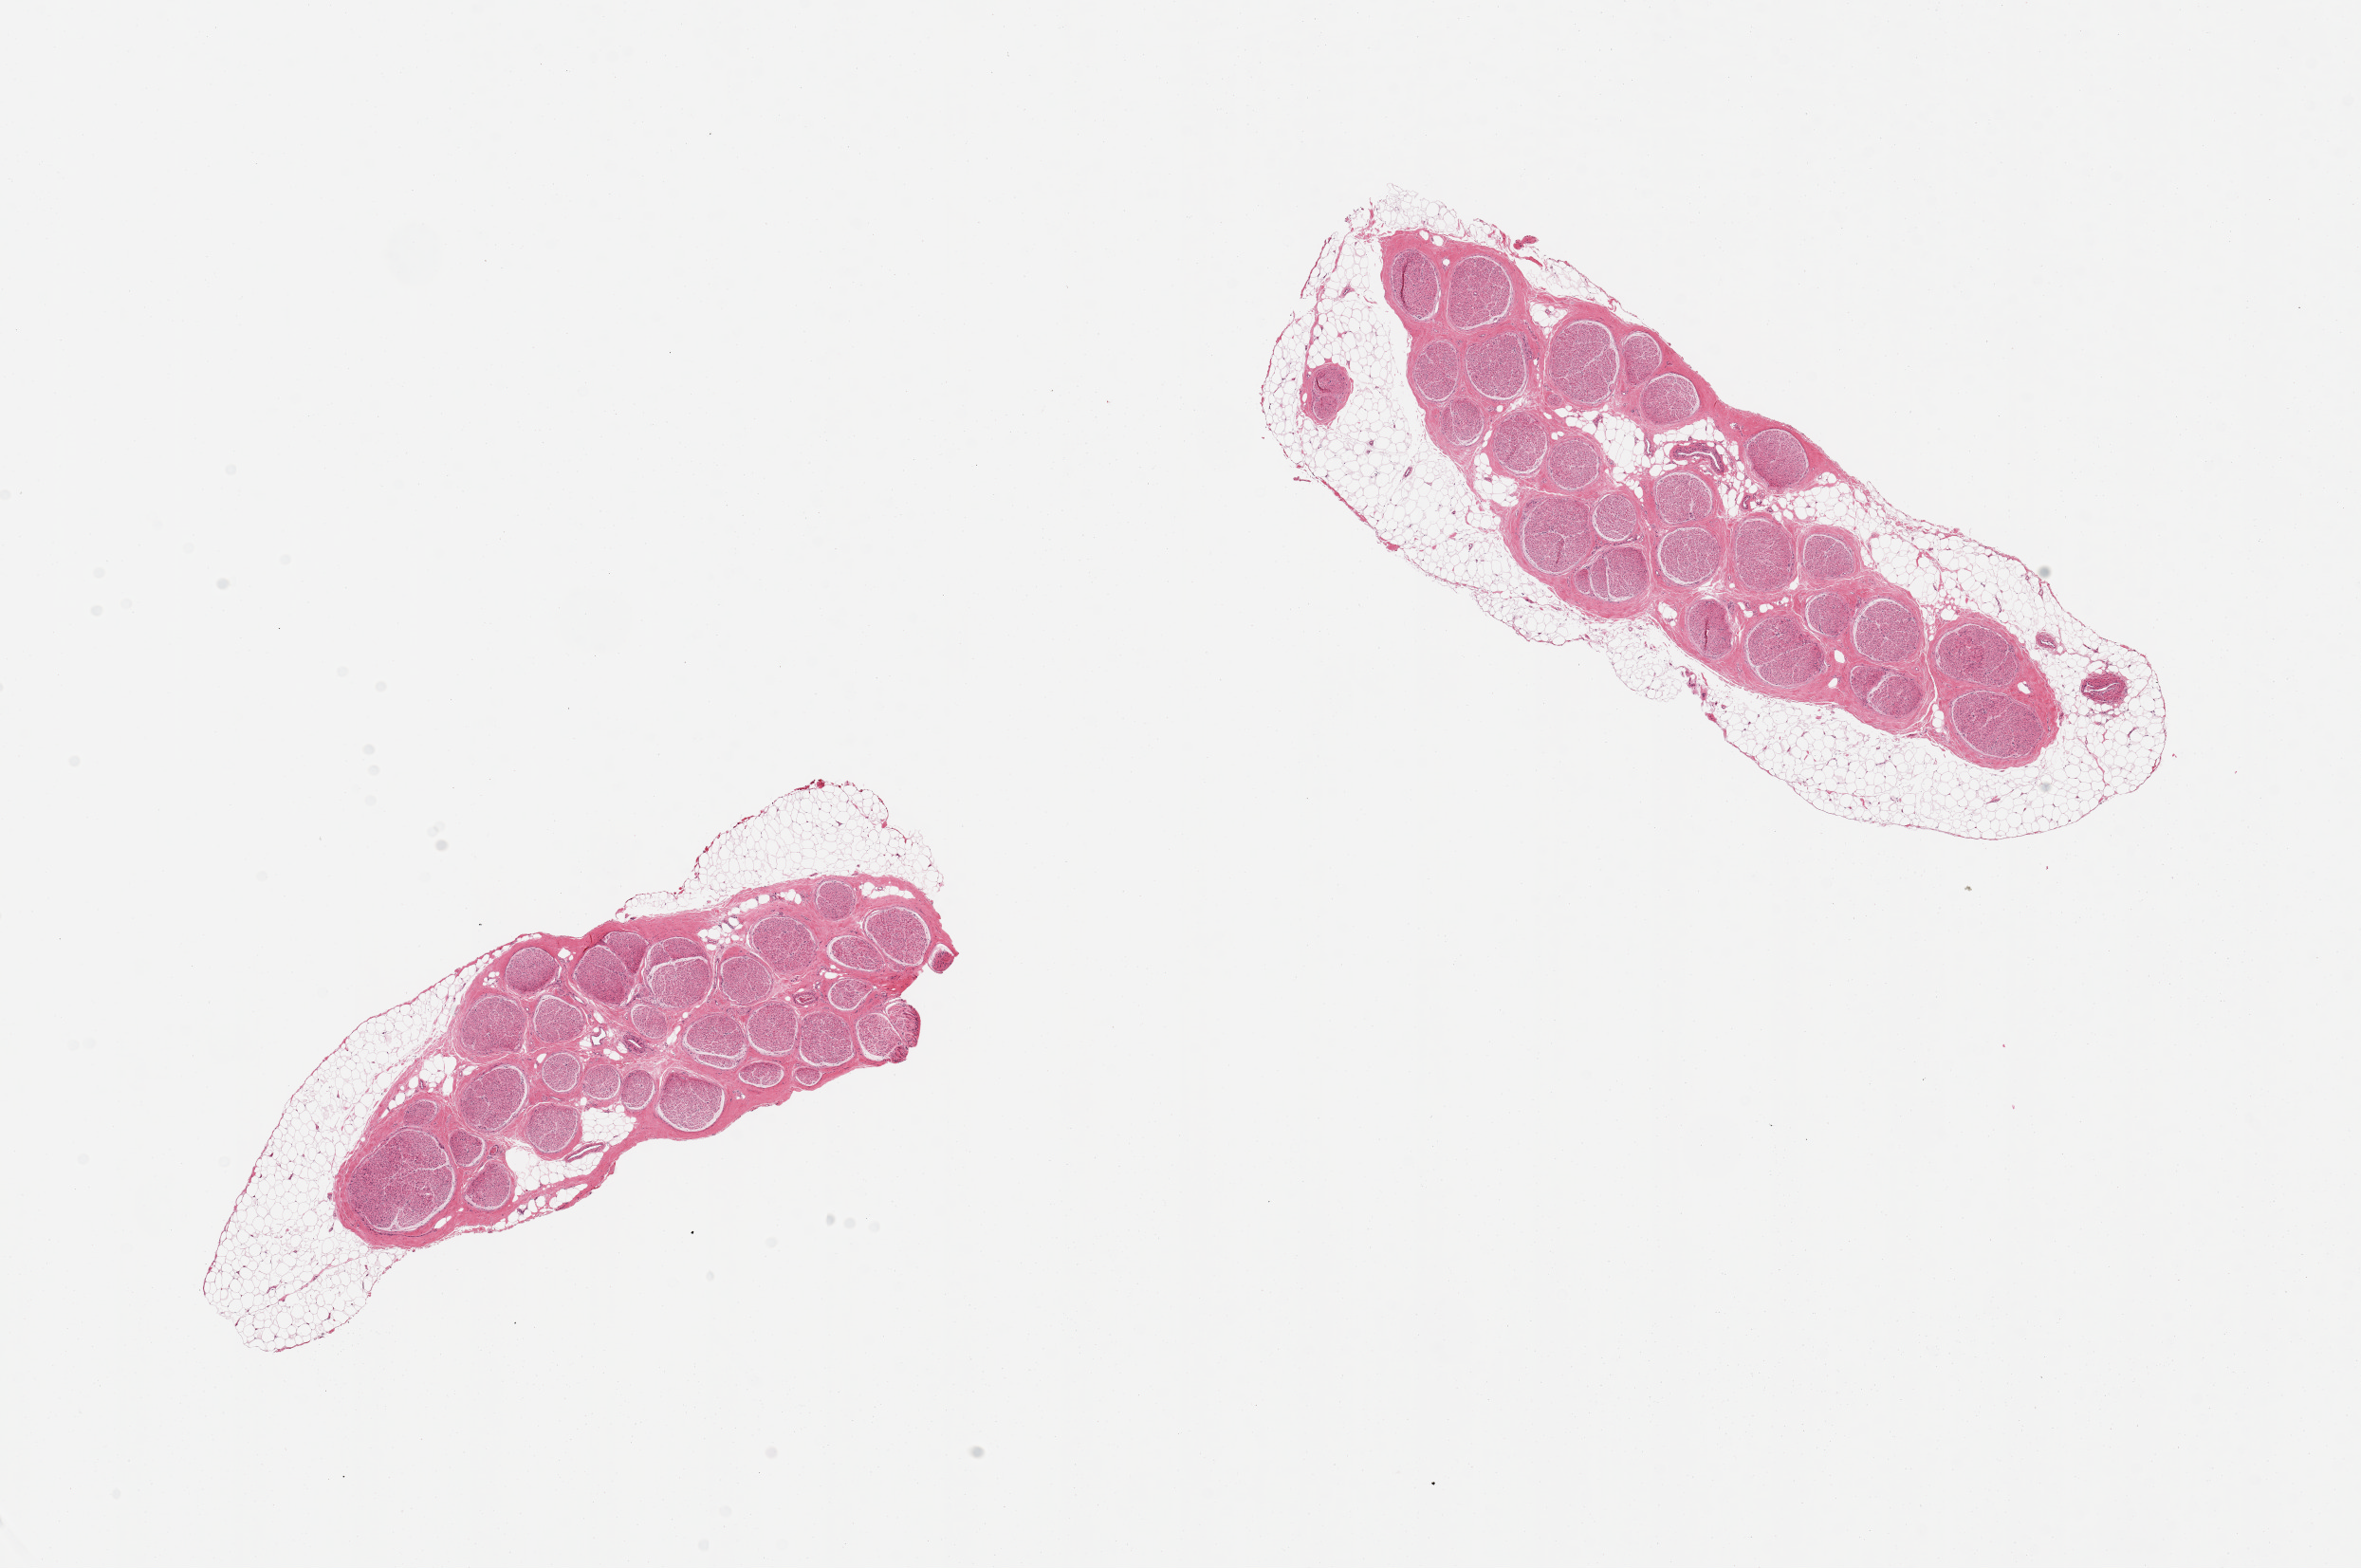
Whole-slide image, hematoxylin and eosin (H&E) stain, a low-resolution overview of the entire scanned area, about 19.7 x 13.1 mm, PAXgene-fixed, paraffin-embedded tissue, target tissue: tibial nerve, donor tissue sample. Donor: male.
Pathologist's review note for this sample: 2 pieces, rim of adherent fat up to ~1mm discontinuous around both setions.